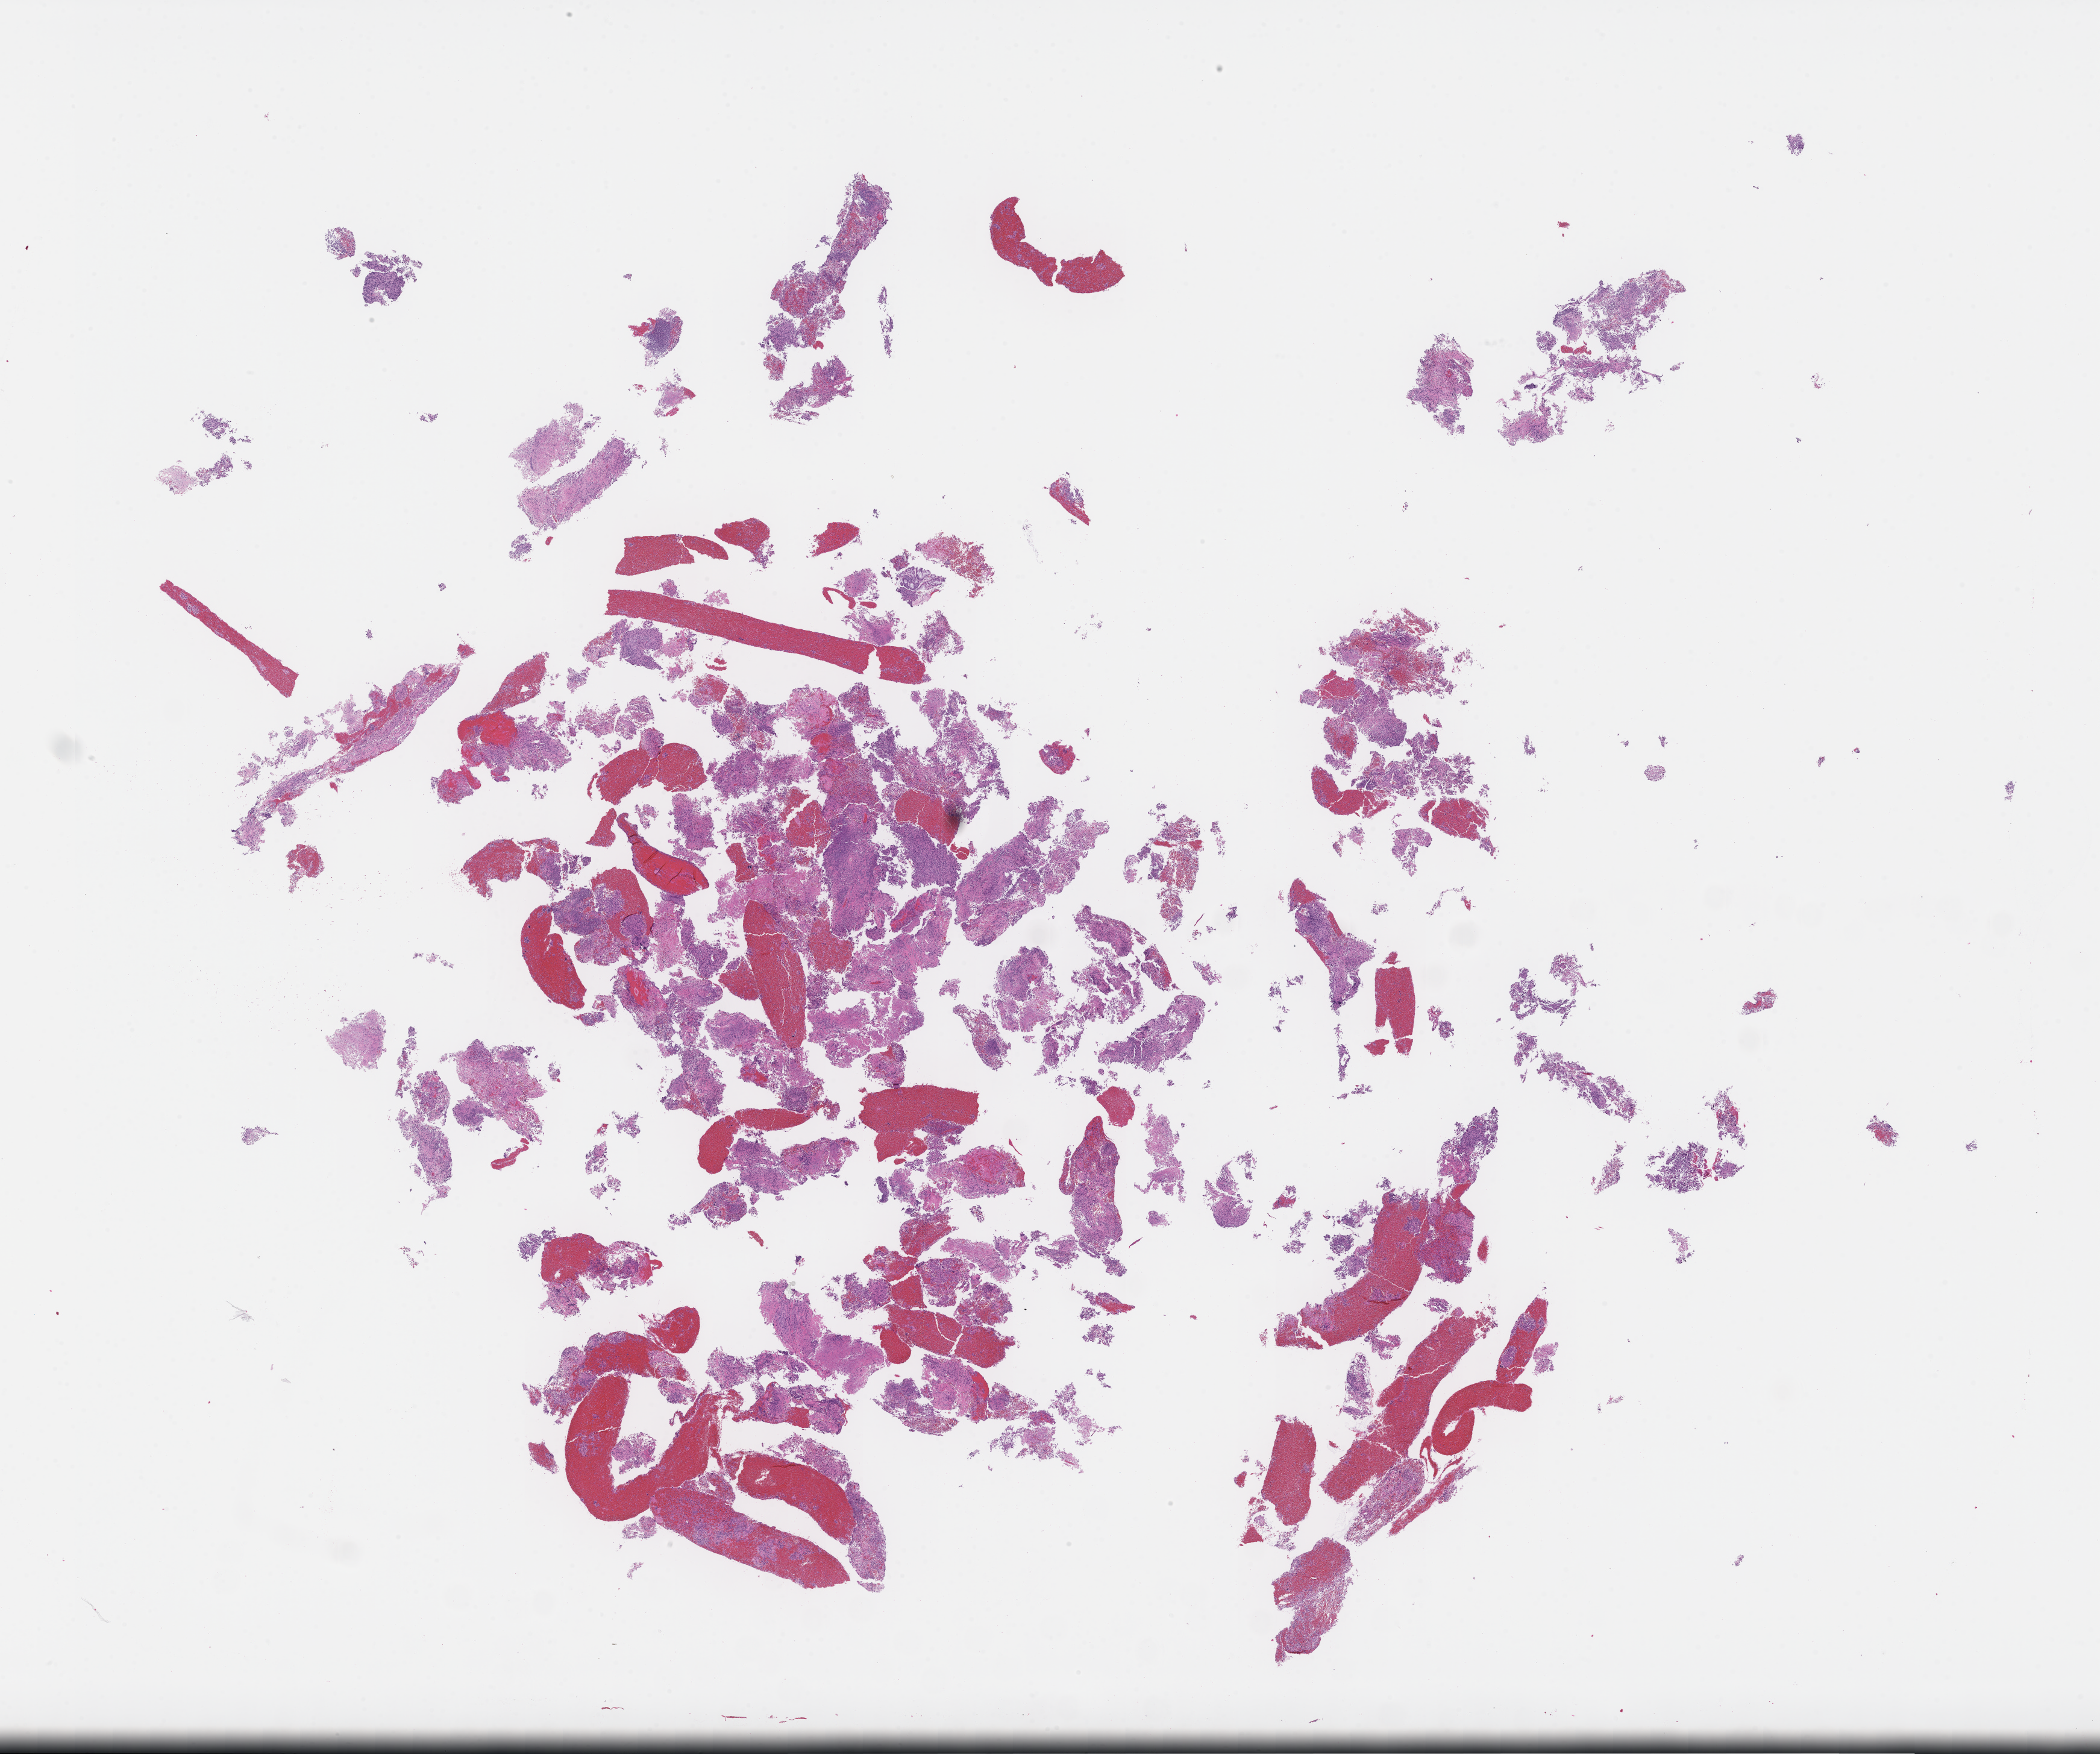
Hematoxylin and eosin (H&E) whole-slide image, shown as a low-resolution overview of the whole scanned area (about 28.1 x 23.5 mm). Formalin-fixed paraffin-embedded section. Archival tissue. Patient: female.
- this section: metastasis (sampled organ not recorded)
- patient diagnosis (primary): Non-Small Cell Lung Carcinoma